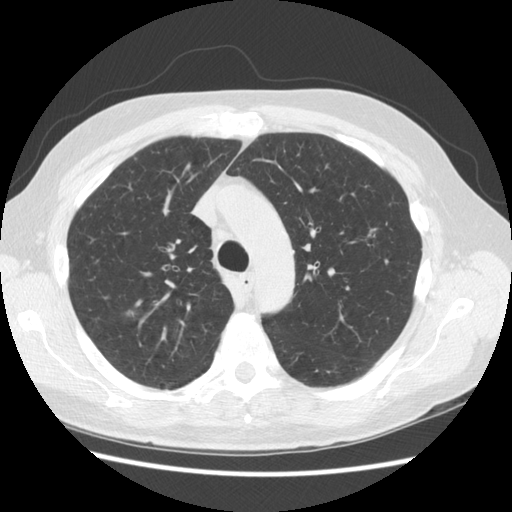
Low-dose screening chest CT, axial slice; third screening round (two years after baseline); lung window (W 1500 / L -600 HU); standard (soft-tissue) reconstruction kernel (STANDARD); slice 113 of 156 in the series; 512 × 512 image matrix. Male participant, aged 68 years at enrolment. Current smoker at enrolment.
Lesion marked by an expert reader, bounding box [x1, y1, x2, y2] px = [111, 296, 155, 333]. Screening reader's record for this exam (one nodule recorded; not confirmed to be the boxed lesion): non-calcified nodule or mass ≥4 mm, right upper lobe, 11 × 9 mm, smooth margins, soft tissue attenuation, pre-existing on the prior screen: yes; interval growth: yes. Lung cancer was diagnosed 246 days after this screen: adenocarcinoma, NOS, right upper lobe, moderately differentiated (G2), stage IA (AJCC 6th edition), 13 mm at pathology.